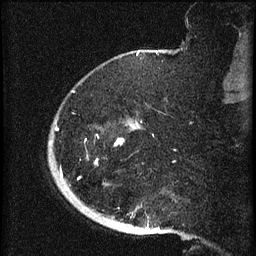
Breast MRI (dynamic contrast-enhanced), one sagittal slice; slice 13 of 60 in the series (ordered by position); dynamic contrast-enhanced series, image 2 of 3 at this slice position (ordered by acquisition); 1.5 T; TE 4.2 ms, TR 8.2 ms; 2 mm slice thickness; 256 × 256 image matrix, field of view 180 × 180 mm. Female patient, age 71 years.
Outlined on this slice (semi-automatic segmentation, software-assisted and operator-edited):
- analysis volume of interest (the breast-tissue region the enhancement analysis was run in; not a lesion): bounding box (x1, y1, x2, y2) in pixels: (48, 73, 140, 196)
- tumour enhancement mask (voxels above the 70 % enhancement threshold inside the analysis volume of interest): (55, 125, 131, 175)